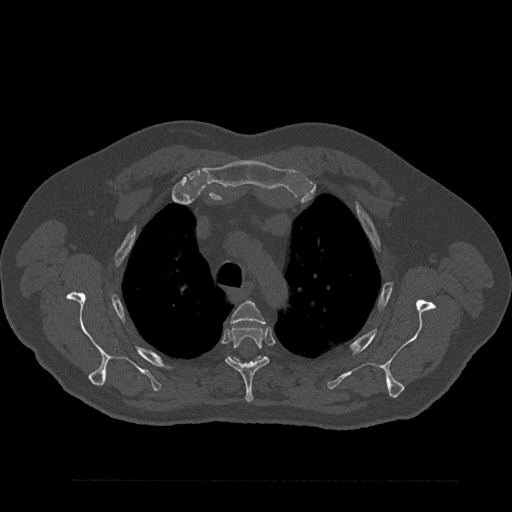
CT including the spine, one axial slice. Position 646 of 797 along the scan axis. Reconstruction kernel Br40s/3. Bone window (W 1800 / L 400 HU). 0.5 mm slice thickness. 512 × 512 image matrix, field of view 430 × 430 mm. Patient: male, 61 years. From the clinical record (not read from this slice): primary cancer: prostate.
Outlined on this slice (semi-automatic segmentation, software-assisted and operator-edited):
- T3 vertebra: bounding box [x1, y1, x2, y2] px = [231, 301, 265, 324]
- T4 vertebra: [225, 325, 270, 402]
- T5 vertebra: [233, 356, 265, 363]